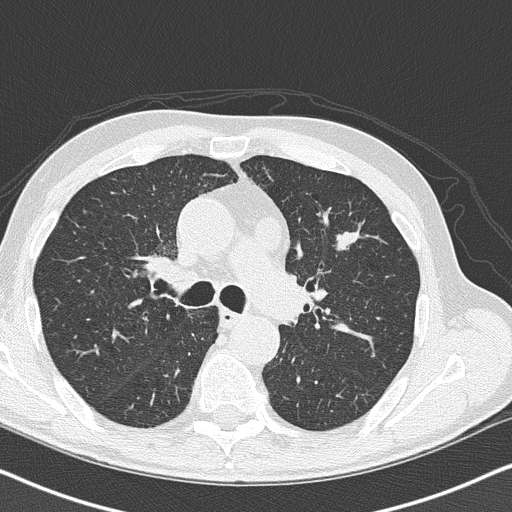
Chest CT (low-dose screening protocol), one axial image, second annual screen, lung window (W 1500 / L -600 HU), lung (sharp) reconstruction kernel (B50f), slice 103 of 158 in the series. Male participant, aged 73 years at enrolment.
Expert-annotated lung lesion, bounding box <313,217,375,269> (left, top, right, bottom; pixels). The screening reader recorded 3 non-calcified nodules or masses ≥4 mm on this exam (left upper lobe, left upper lobe, right lower lobe); which of them this box marks is not recorded. Official screen result: positive, other.